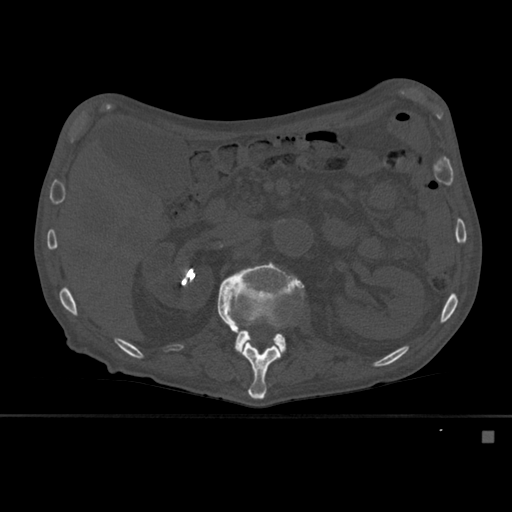
CT including the spine, one axial slice. Position 247 of 527 along the scan axis. Bone window (W 1800 / L 400 HU). 1.5 mm slice thickness. 512 × 512 image matrix, field of view 373 × 373 mm. Male patient, age 78 years. From the clinical record (not read from this slice): primary cancer: prostate.
Structures marked on this image (semi-automatically segmented with operator editing):
- L1 vertebra: bounding box <221,284,293,400> (left, top, right, bottom; pixels)
- L2 vertebra: <217,262,304,355>